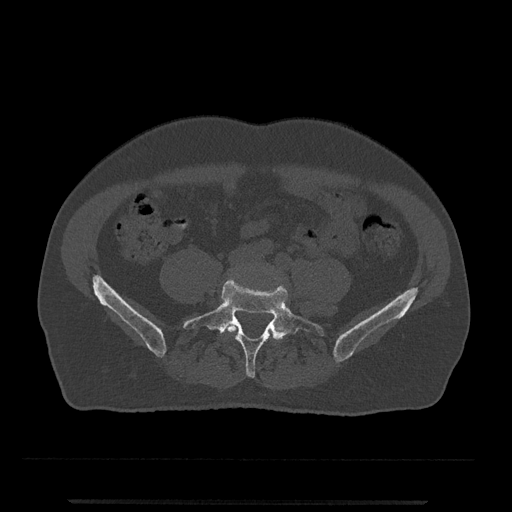
CT including the spine, one axial slice. Slice 84 of 797 in the series (ordered by position). 120 kVp. Bone window (W 1800 / L 400 HU). 0.5 mm slice thickness. 512 × 512 image matrix. Male patient, age 63 years. From the clinical record (not read from this slice): primary cancer: prostate.
Annotated regions visible in this slice (semi-automatic segmentation, software-assisted and operator-edited):
- L4 vertebra: bounding box (x1, y1, x2, y2) in pixels: (224, 322, 273, 333)
- L5 vertebra: (183, 279, 324, 378)